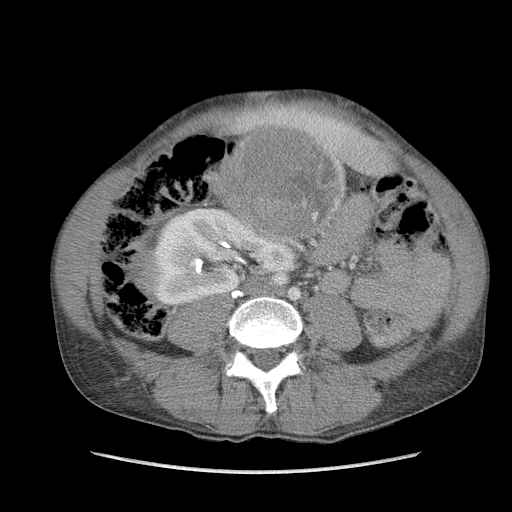
Contrast-enhanced abdominal CT, one axial slice. Position 41 of 115 along the scan axis. Soft-tissue window (W 400 / L 40 HU). 5 mm slice thickness. 512 × 512 image matrix, field of view 360 × 360 mm. Male patient. Case-level facts recorded for this patient, not image findings: diagnosis: adrenocortical carcinoma; tumour side: right adrenal; Ki-67 index: 13 %; stage (as recorded): 3.
Annotated regions visible in this slice (semi-automatically segmented with operator editing):
- mass: bounding box <228,130,336,230> (left, top, right, bottom; pixels)